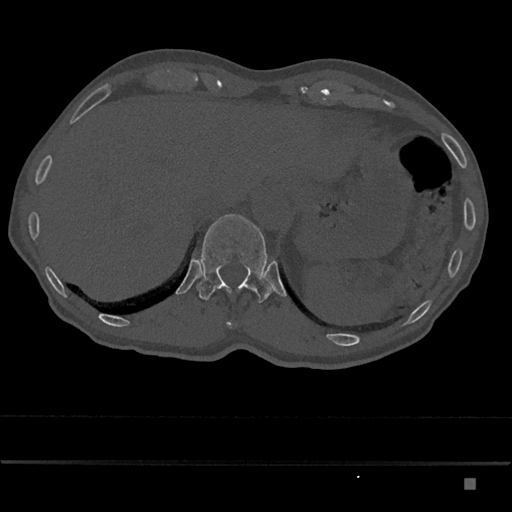
CT including the spine, one axial slice. Slice 625 of 797 in the series (ordered by position). Reconstruction kernel Br40s/3. 120 kVp. Bone window (W 1800 / L 400 HU). 0.5 mm slice thickness. 512 × 512 image matrix, field of view 390 × 390 mm. Male patient, age 72 years. From the clinical record (not read from this slice): primary cancer: prostate.
Annotated regions visible in this slice (semi-automatic segmentation, software-assisted and operator-edited):
- T11 vertebra: bounding box <226,322,232,328> (left, top, right, bottom; pixels)
- T12 vertebra: <196,214,273,303>